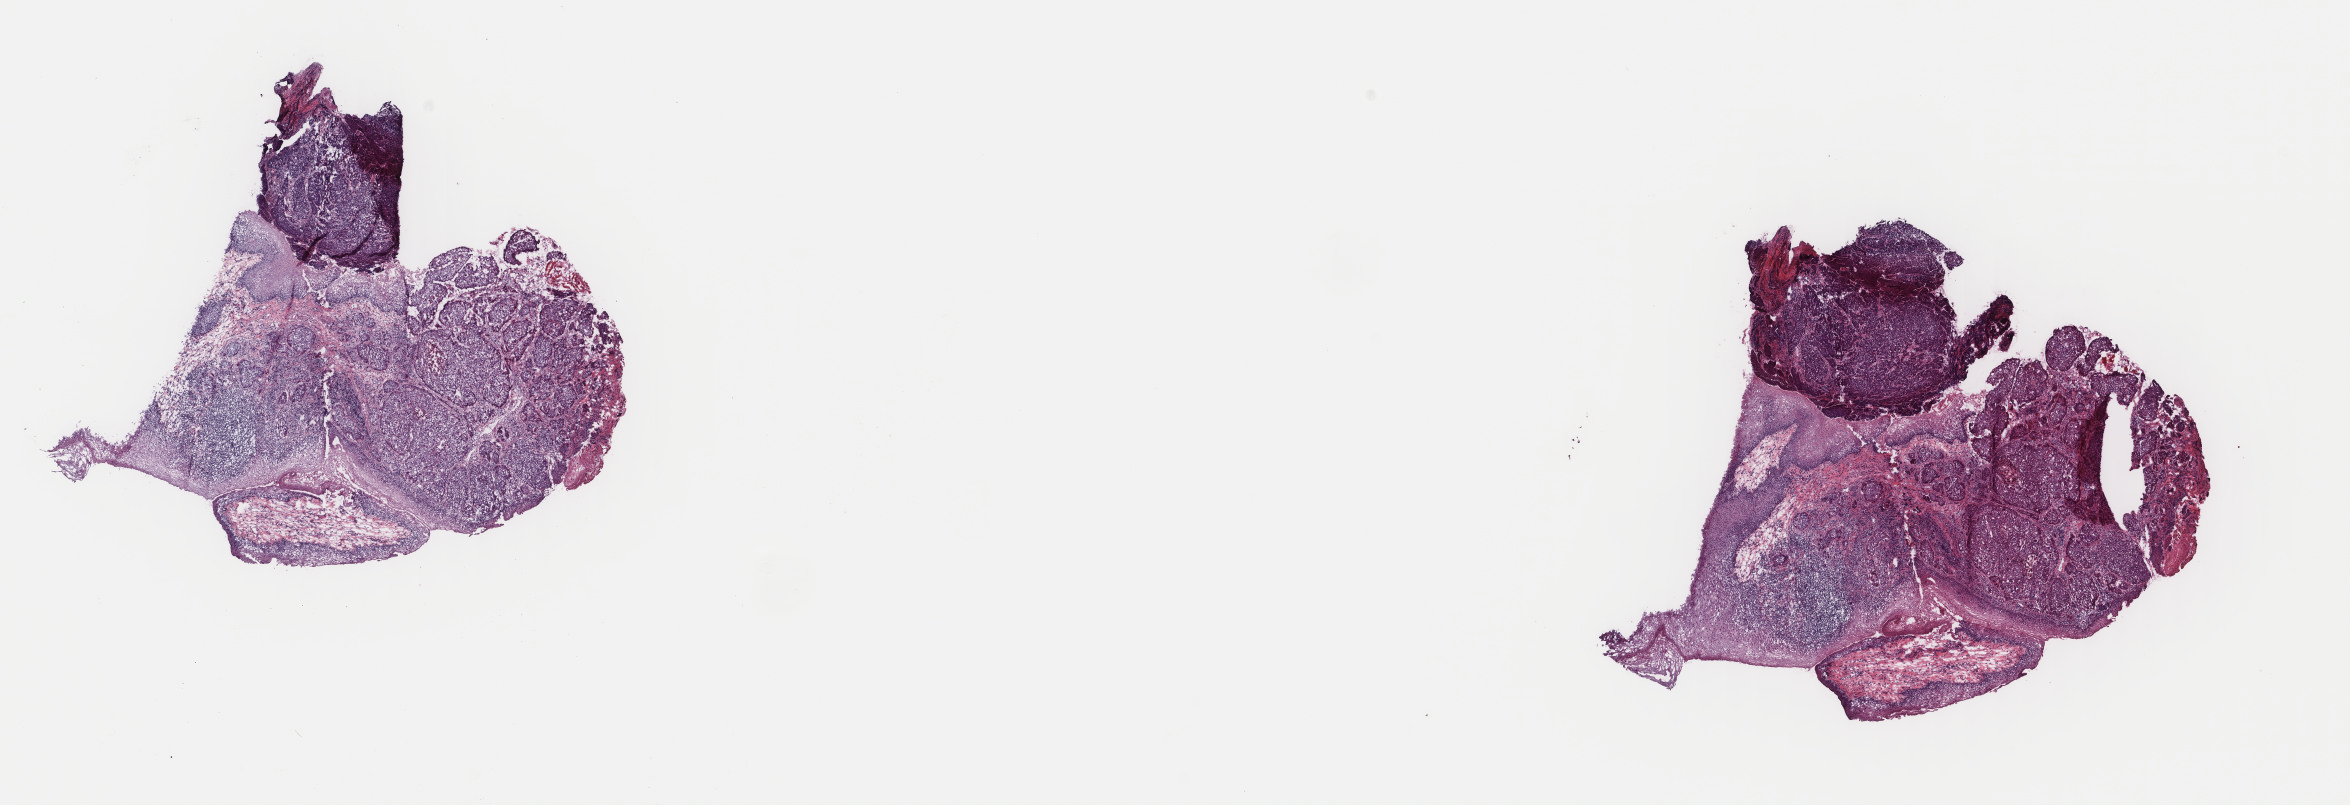
Whole-slide histology image, Hematoxylin and eosin (H&E) stained, a low-resolution overview of the entire scanned area, about 18.7 x 6.4 mm. Frozen section. Head and neck, primary tumour sample. Male patient; age at initial diagnosis 68 years.
Diagnosis: Squamous cell carcinoma, NOS (oropharynx, NOS).